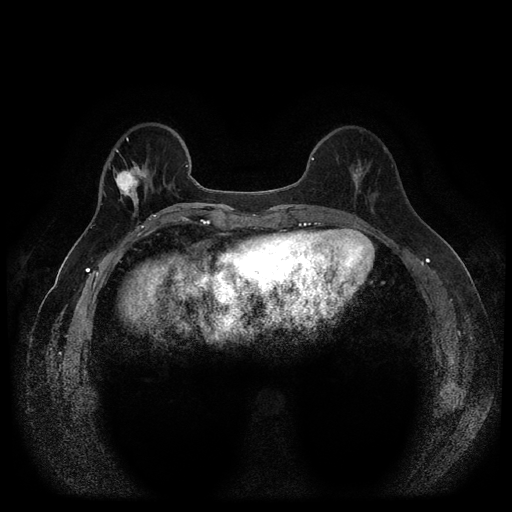
Breast MRI (dynamic contrast-enhanced, multi-phase), one axial slice. Position 32 of 116 along the scan axis. Dynamic contrast-enhanced series, time point 2 of 5 at this slice position (early post-contrast). 1.5 T. TE 2.6 ms, TR 5.4 ms. 2 mm slice thickness. 512 × 512 image matrix, field of view 340 × 340 mm. Patient: female, 56 years.
Structures marked on this image (semi-automatically segmented with operator editing):
- breast lesion (labelled 'tumour' in the annotation; benign lesions carry a separate 'benign' label): bounding box (x1, y1, x2, y2) in pixels: (113, 158, 152, 219)